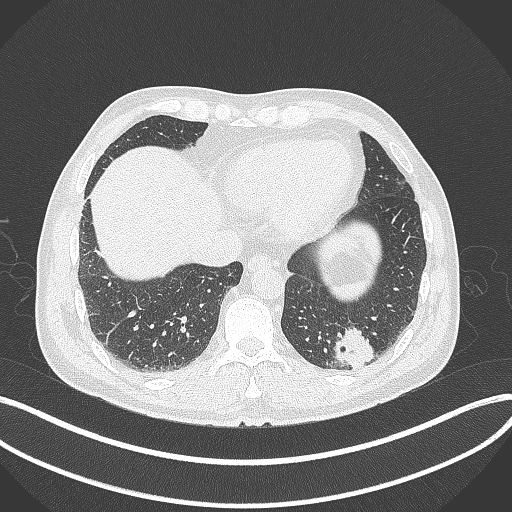
Chest CT, one axial slice. Slice 66 of 300 in the series (ordered by position). 120 kVp. Lung window (W 1500 / L -600 HU). 1 mm slice thickness. 512 × 512 image matrix, field of view 400 × 400 mm. Male patient, age 54 years. From the clinical record (not read from this slice): clinical TNM (as recorded): T1c N0 M1.
Structures marked on this image (rectangle marked by the reading radiologist):
- lung tumour (recorded histology: adenocarcinoma): box from (x=333, y=322) to (x=377, y=376) px